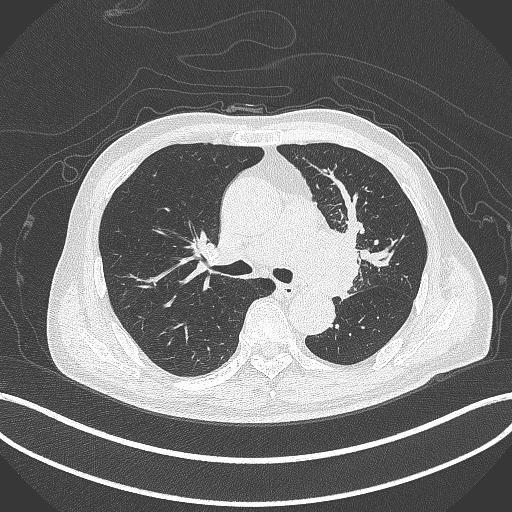
Chest CT, one axial slice; slice 270 of 417 in the series (ordered by position); lung window (W 1500 / L -600 HU); 1 mm slice thickness; 512 × 512 image matrix, field of view 400 × 400 mm. Patient: male, 77 years. Case-level facts recorded for this patient, not image findings: clinical TNM (as recorded): T3 N1 M0.
Outlined on this slice (rectangle marked by the reading radiologist):
- lung tumour (recorded histology: adenocarcinoma): bounding box [x1, y1, x2, y2] px = [315, 223, 362, 296]